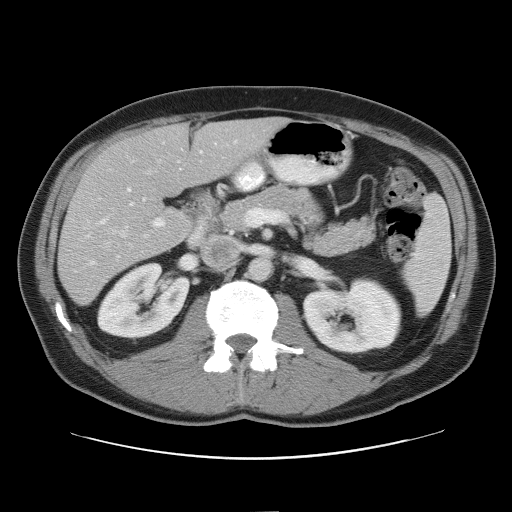
Contrast-enhanced abdominal CT, one axial slice. Reconstruction kernel STANDARD. Soft-tissue window (W 400 / L 40 HU). 512 × 512 image matrix, field of view 393 × 393 mm. Male patient, age 70 years. Case-level facts recorded for this patient, not image findings: diagnosis: colorectal cancer liver metastases, imaged before liver resection; multiple liver metastases: yes; largest metastasis: 4 cm; disease in both lobes: yes.
Structures marked on this image (expert manual segmentation):
- hepatic veins: box from (x=80, y=160) to (x=161, y=267) px
- liver: (x=59, y=117)–(x=284, y=304)
- planned liver remnant (the part of the liver to remain after resection): (x=115, y=117)–(x=284, y=190)
- portal vein (with intrahepatic branches): (x=127, y=141)–(x=236, y=228)